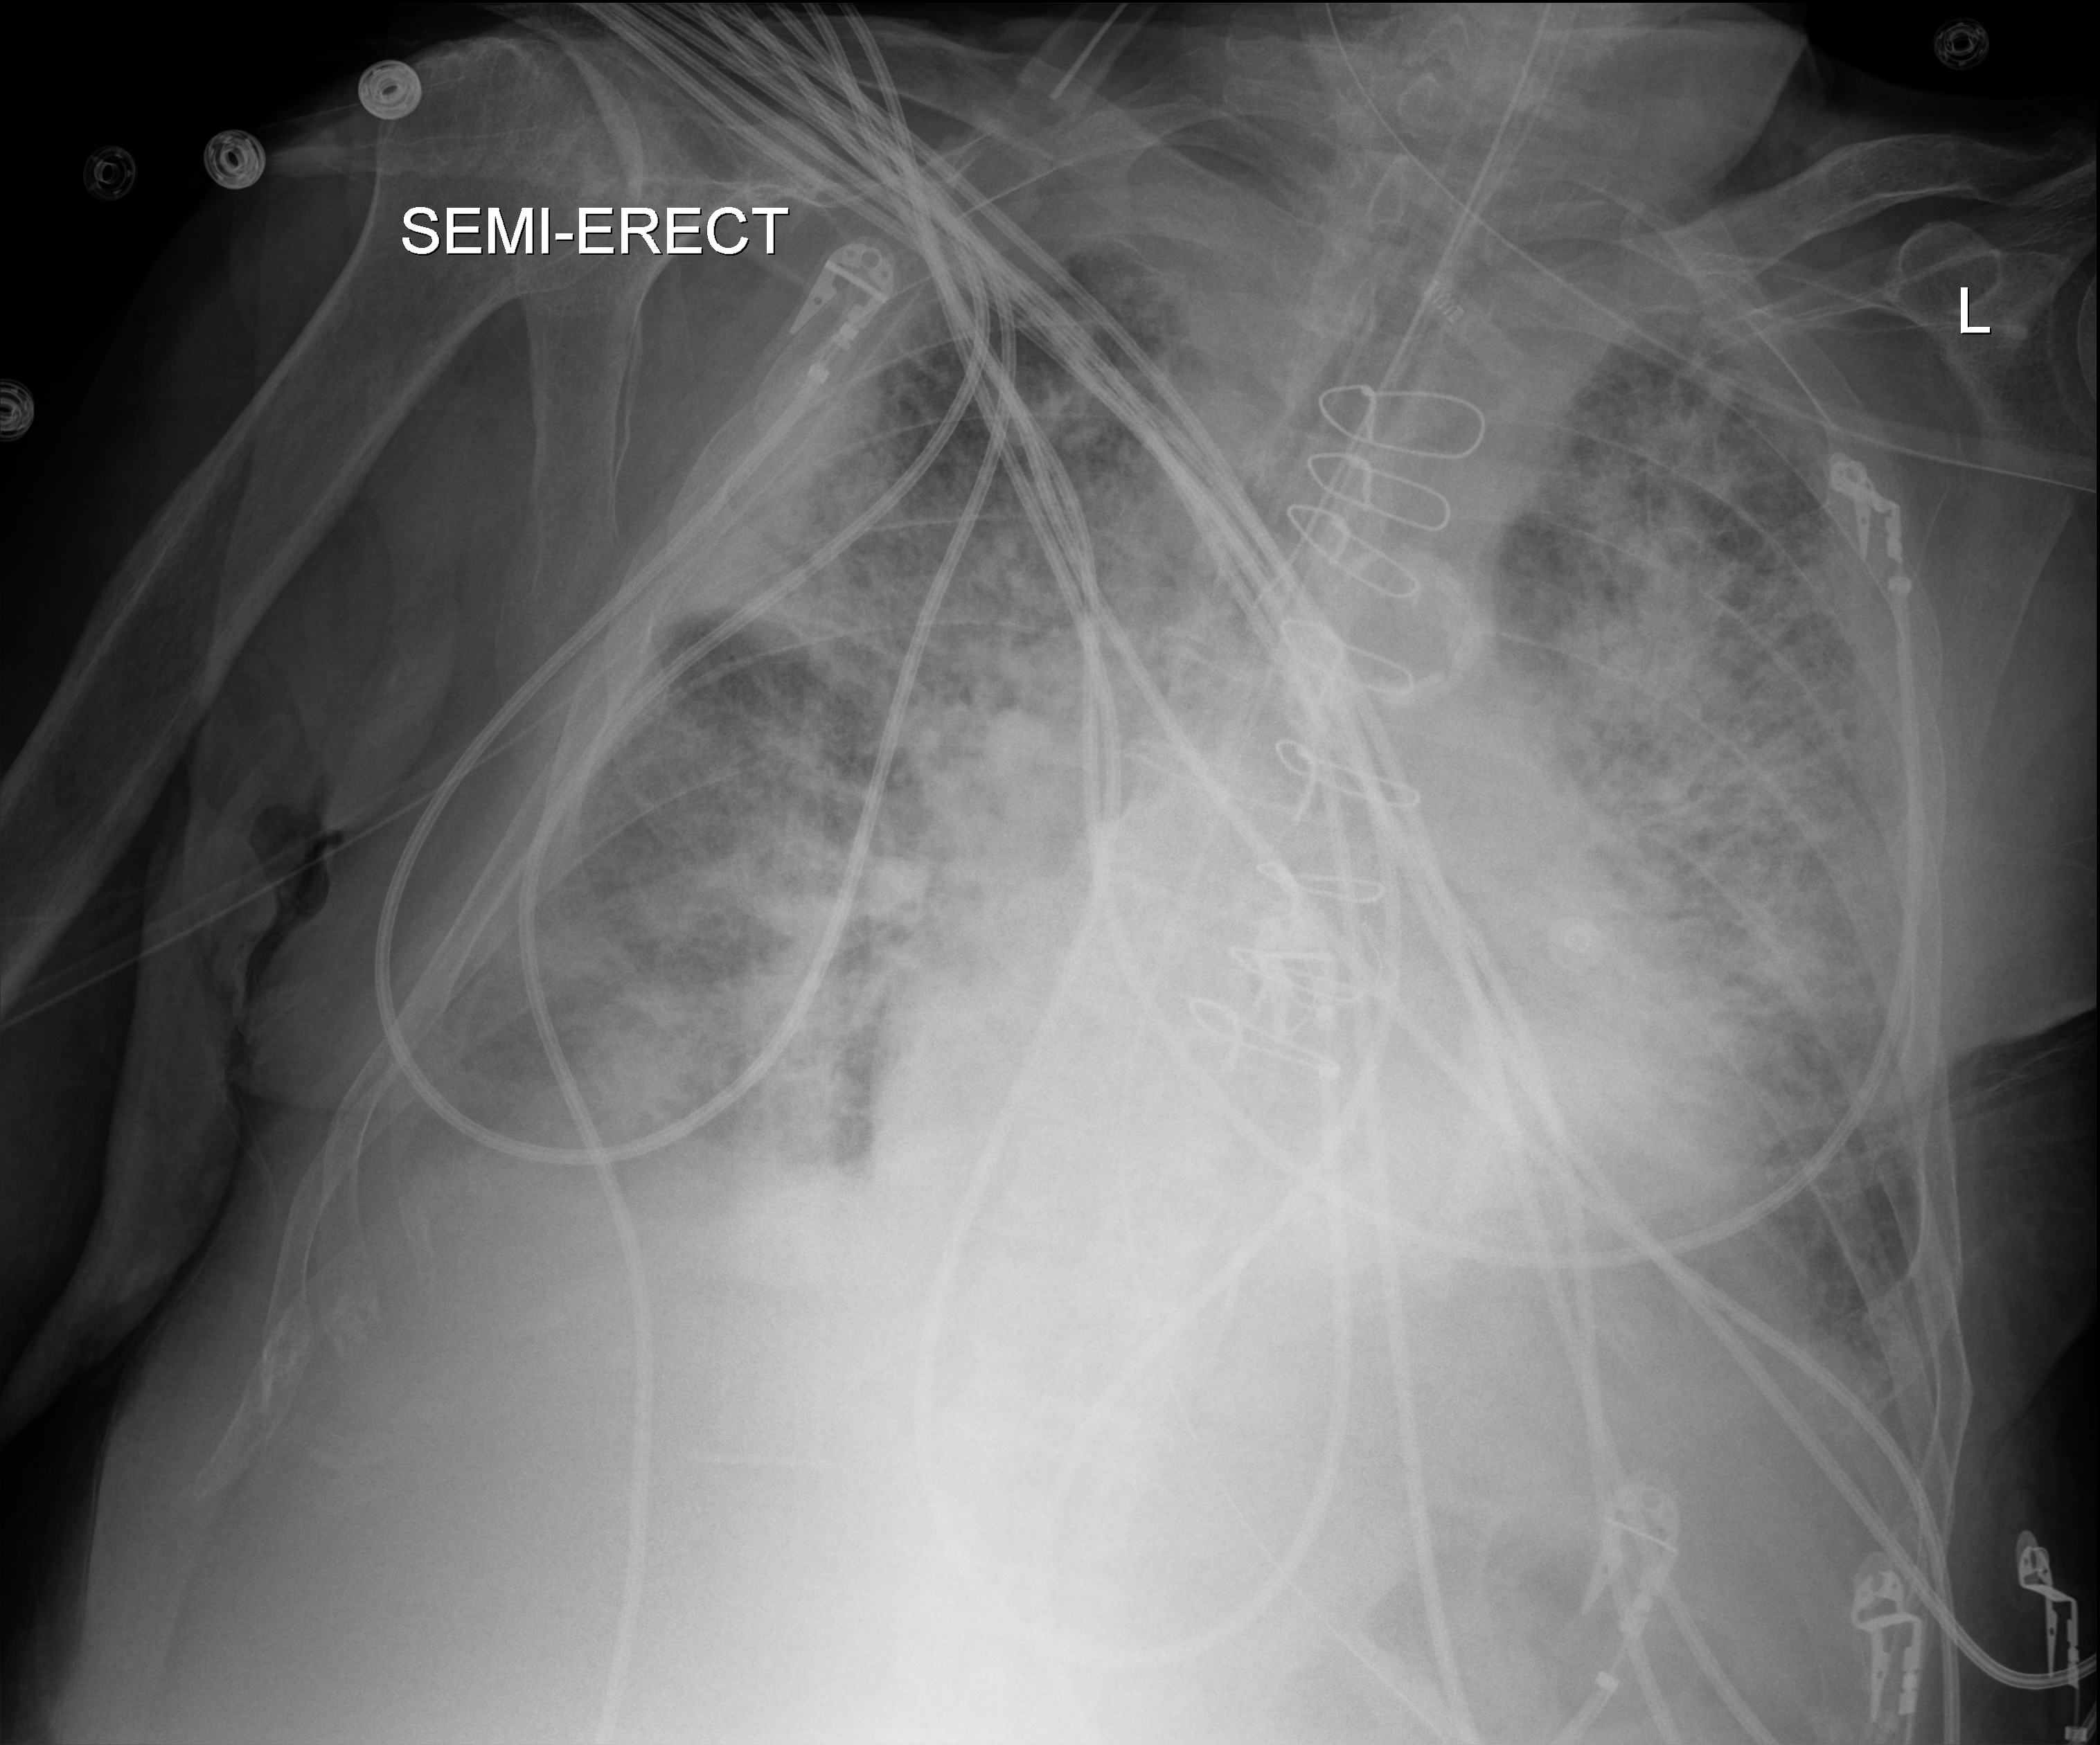
Portable chest radiograph, anteroposterior (AP) projection. Male patient hospitalised with COVID-19, age 75–90 years.
Admission-level facts for this patient (not findings on this image; timing relative to this image not recorded): admitted to intensive care during this hospital stay: yes; mechanically ventilated during this hospital stay: yes.